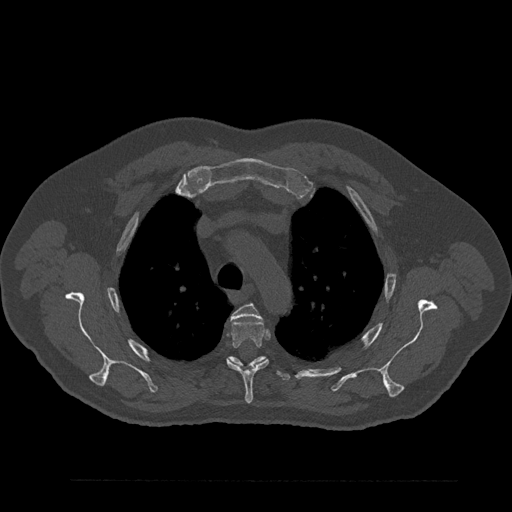
CT including the spine, one axial slice; position 639 of 797 along the scan axis; reconstruction kernel Br40s/3; 120 kVp; bone window (W 1800 / L 400 HU); 512 × 512 image matrix, field of view 430 × 430 mm. Male patient, age 61 years. From the clinical record (not read from this slice): primary cancer: prostate.
Structures marked on this image (semi-automatic segmentation, software-assisted and operator-edited):
- T3 vertebra: bounding box (x1, y1, x2, y2) in pixels: (231, 303, 260, 320)
- T4 vertebra: (226, 320, 269, 404)
- T5 vertebra: (229, 356, 291, 381)